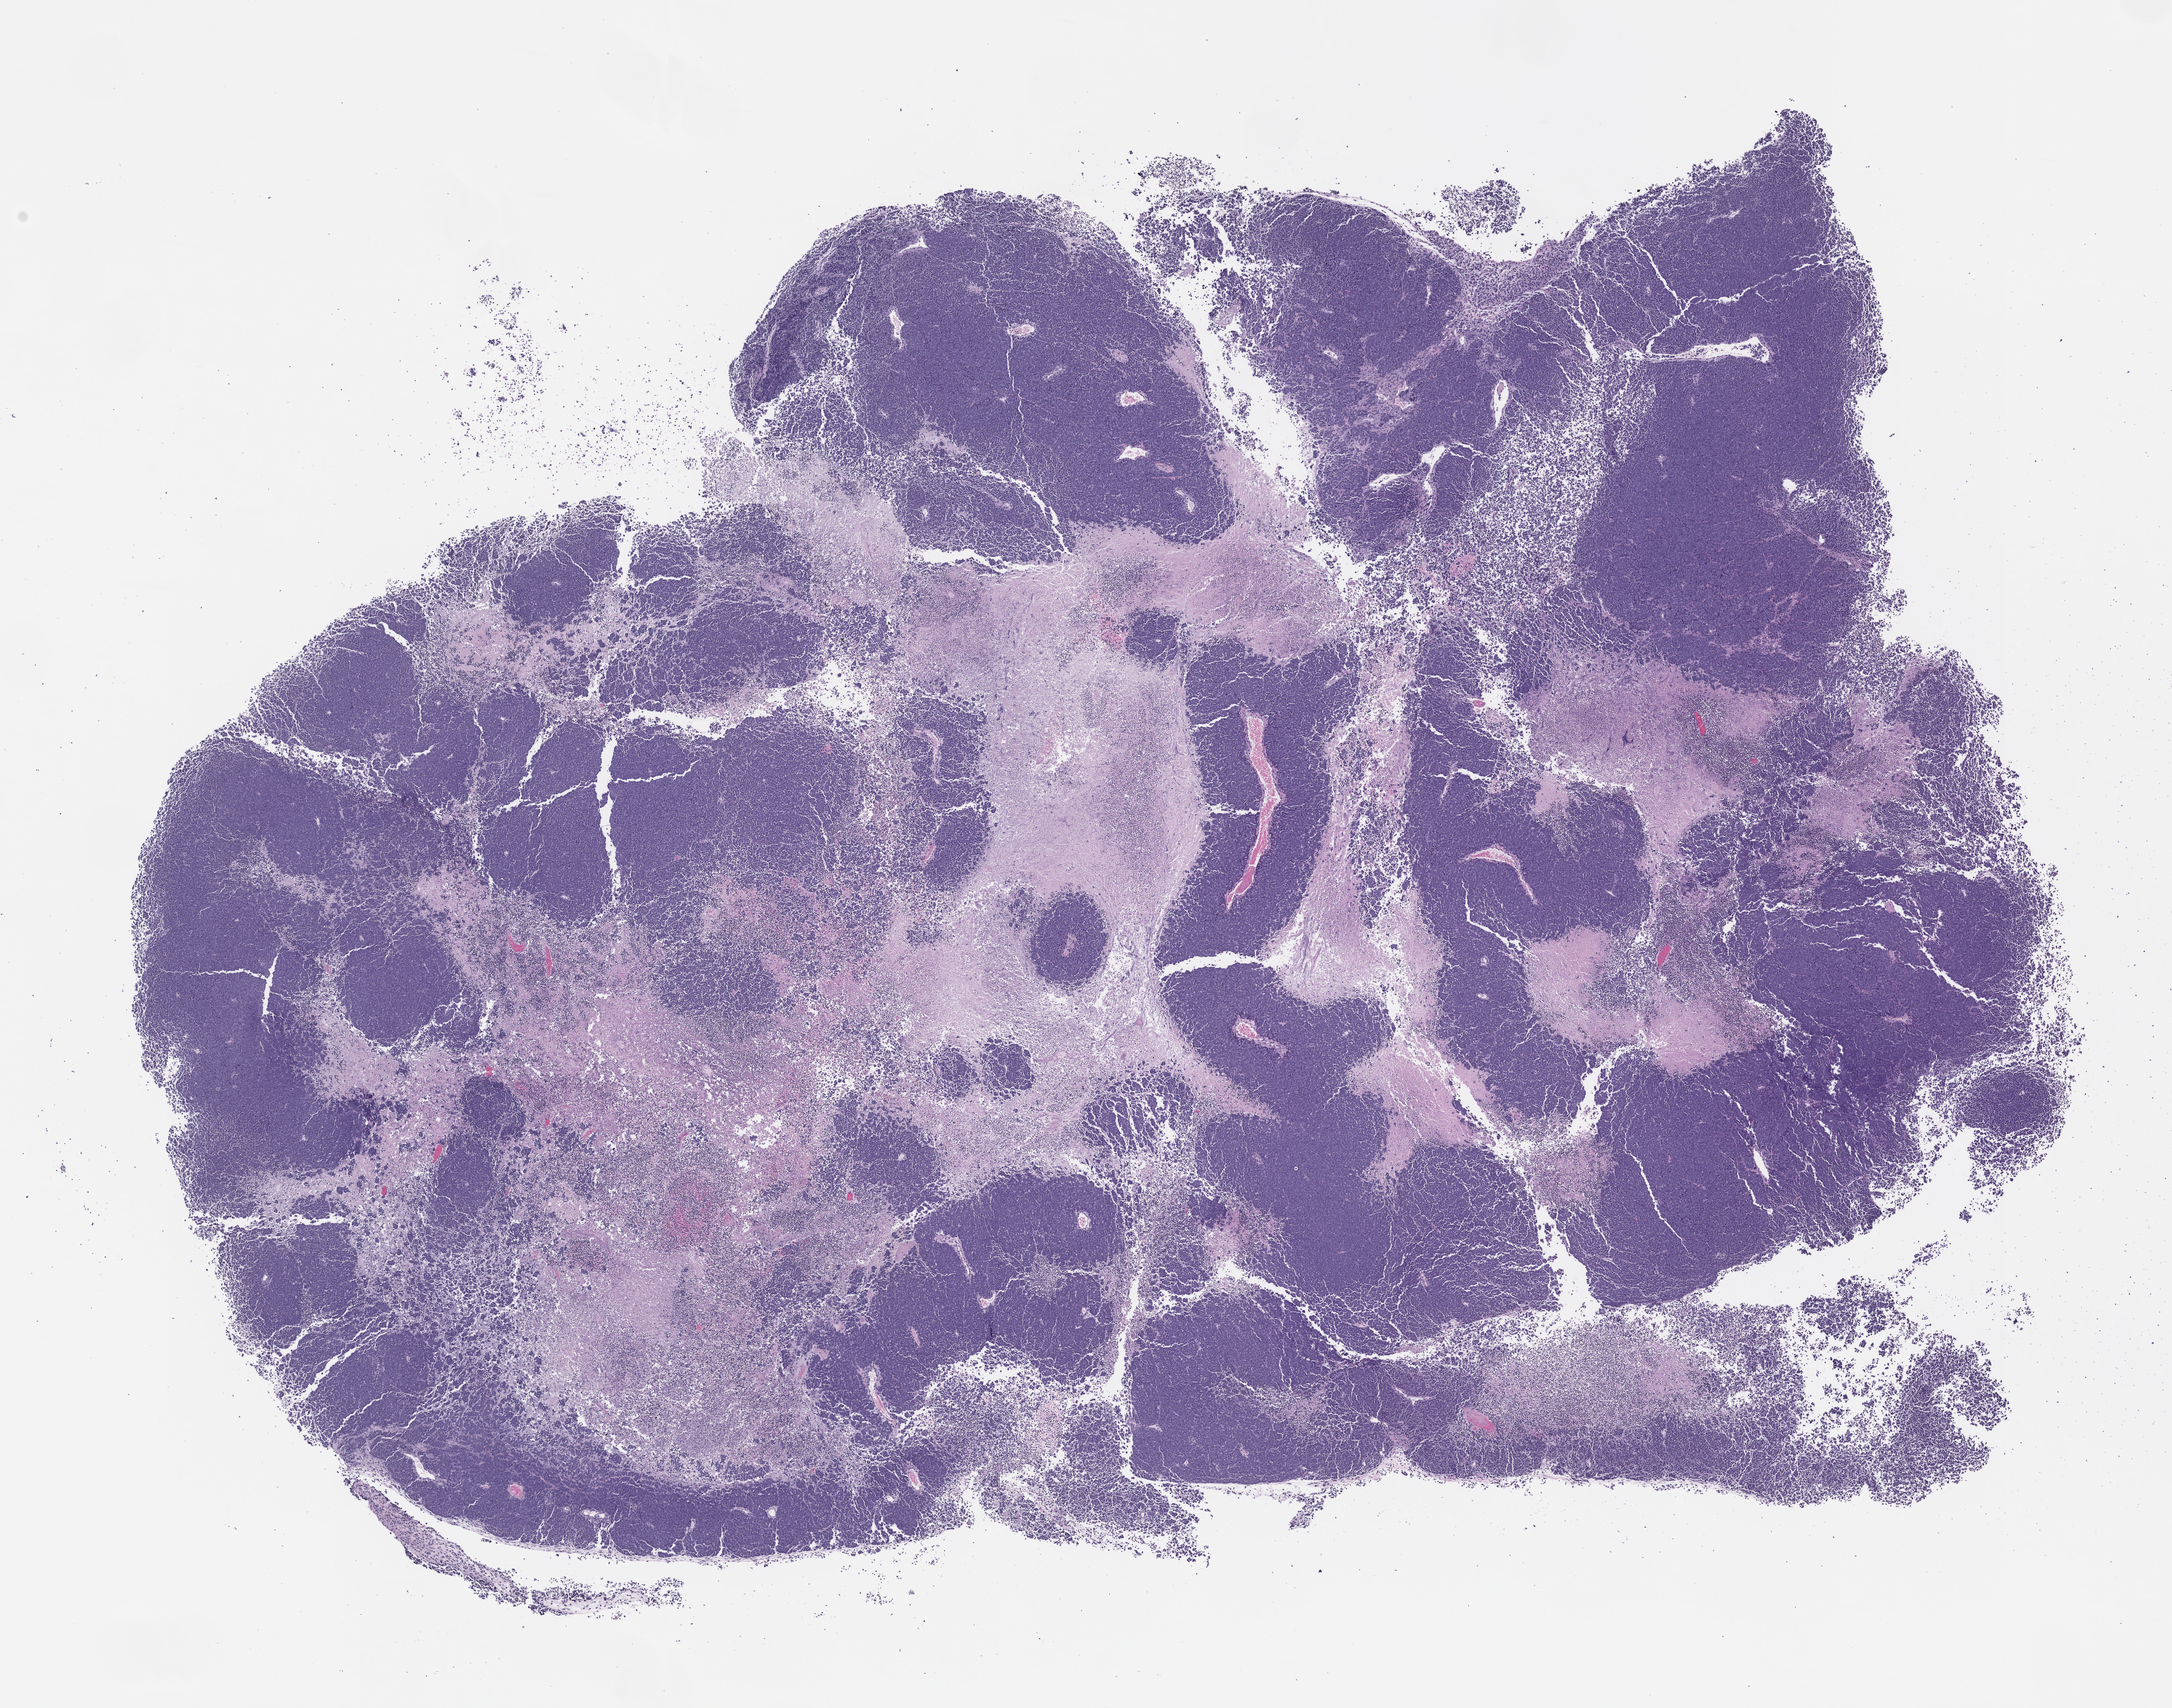
Whole-slide image, H&E: patient-derived xenograft (human tumor grown in a mouse), passage 1 — shown as a low-resolution overview of the whole scanned area (about 13.0 x 10.2 mm), formalin-fixed paraffin-embedded section, originating tumor site category: endocrine.
Originating patient diagnosis: Merkel Cell Carcinoma.